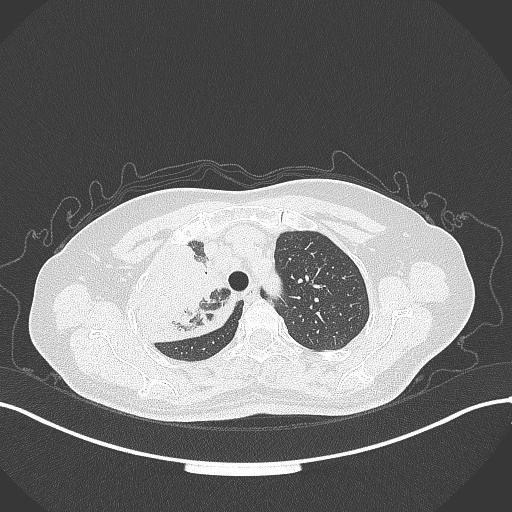
Chest CT, one axial slice. Slice 248 of 309 in the series (ordered by position). Reconstruction kernel B70f. 120 kVp. Lung window (W 1500 / L -600 HU). 1 mm slice thickness. 512 × 512 image matrix, field of view 400 × 400 mm. Female patient, age 60 years. Case-level facts recorded for this patient, not image findings: clinical TNM (as recorded): T3 N1 M1.
Structures marked on this image (rectangle marked by the reading radiologist):
- lung tumour (recorded histology: adenocarcinoma): bounding box [x1, y1, x2, y2] px = [133, 234, 241, 345]